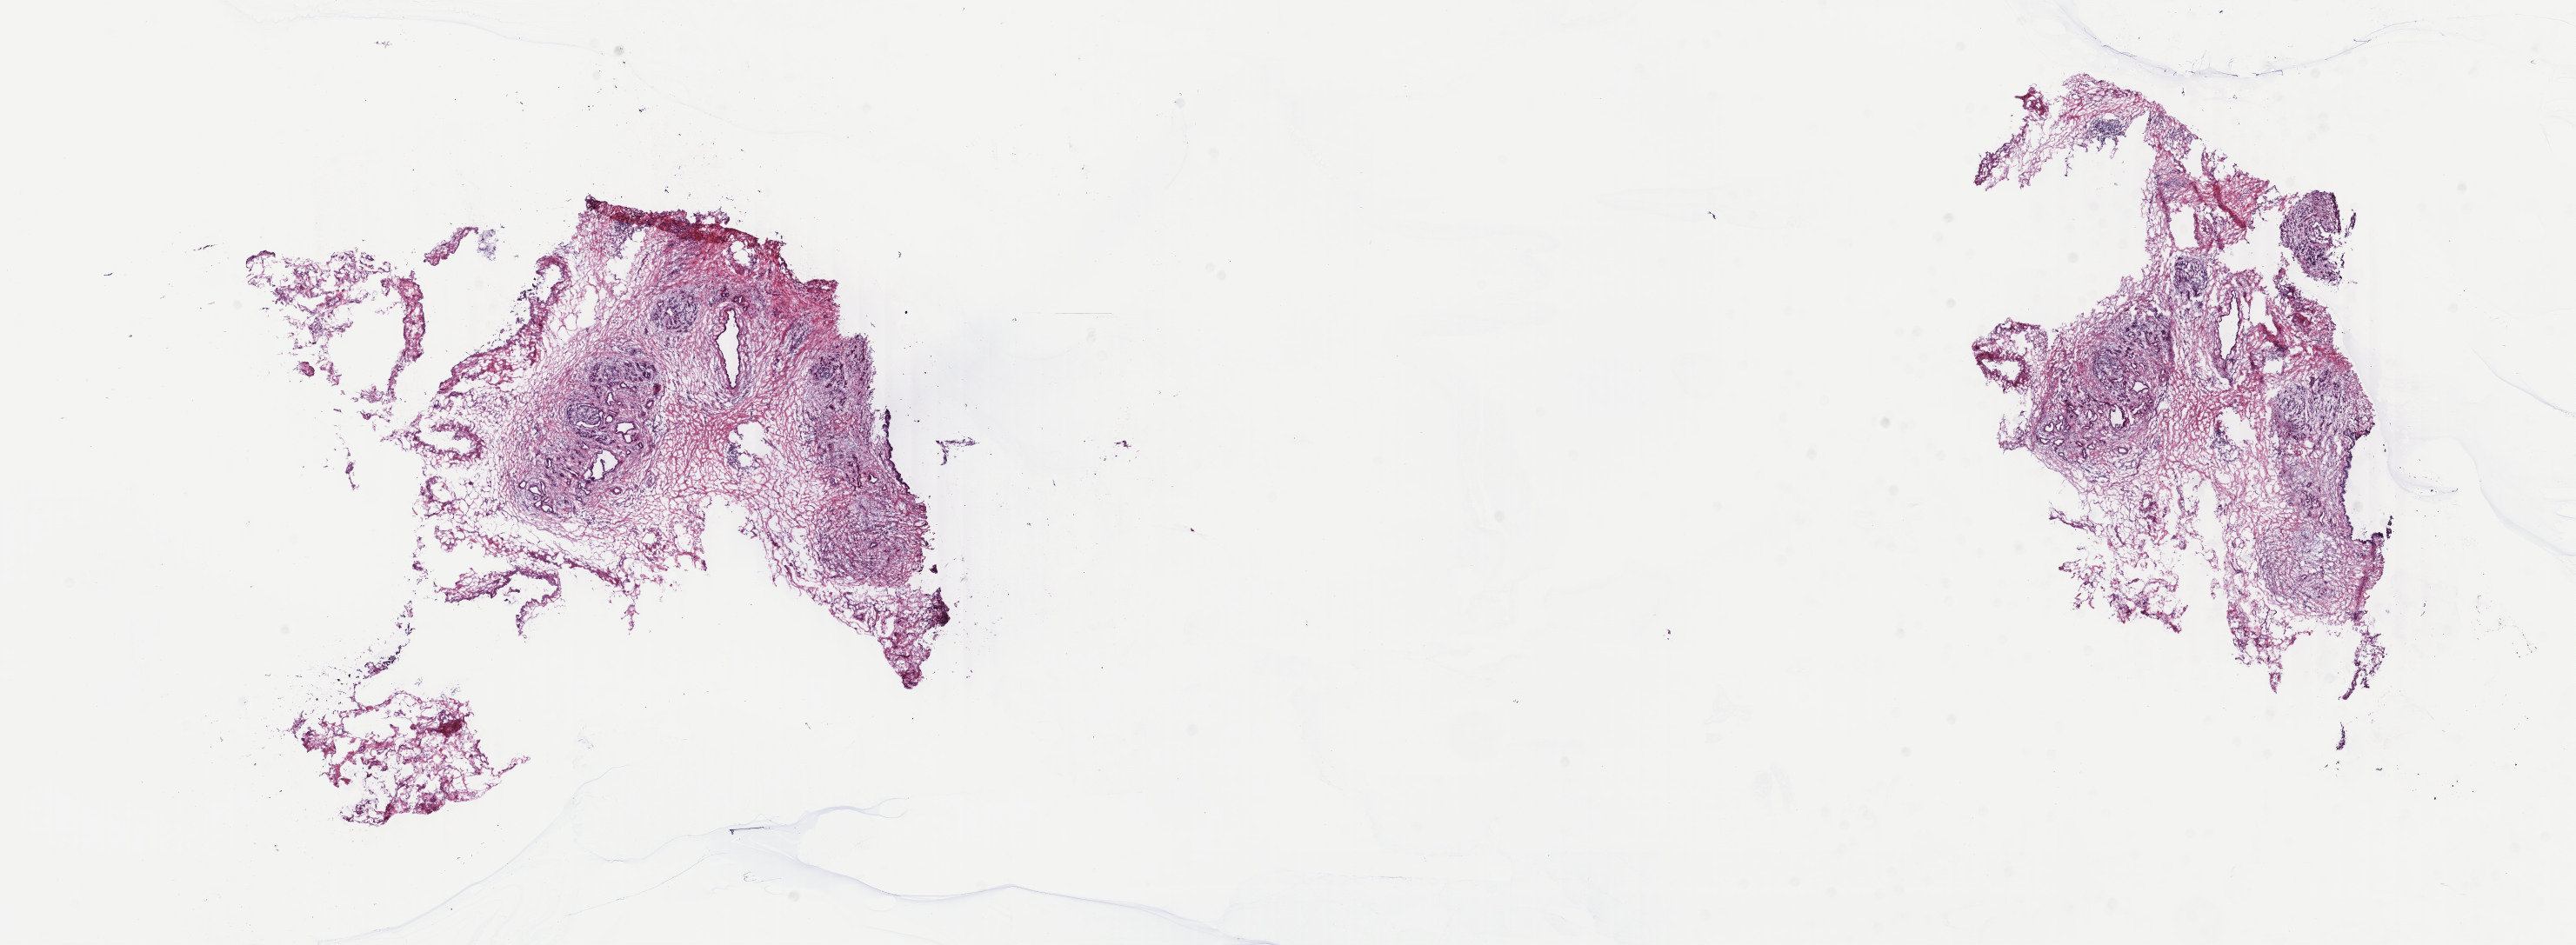
H&E whole-slide image, shown as a low-resolution overview of the whole scanned area (about 23.6 x 8.6 mm), frozen section, primary tumour sample from the pancreas. Patient: female, age at initial diagnosis 63 years. Histologic grade: G3 (poorly differentiated). Slide review estimates, as recorded: tumour cells 2%, tumour nuclei 2%, normal cells 98%, stromal cells 0%, necrosis 0%. Infiltration values recorded for this section: lymphocyte infiltration 15%, monocyte infiltration 0%, neutrophil infiltration 0%.
AJCC pathologic stage: IIB. Diagnosis: Infiltrating duct carcinoma, NOS (head of pancreas). Lymph nodes positive (case pathology): 1 of 9 examined.